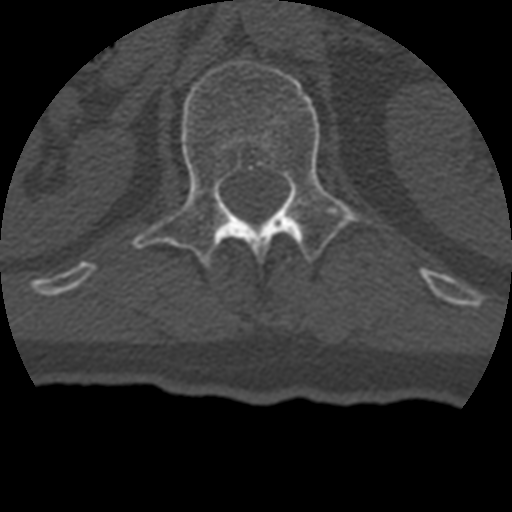
CT including the spine, one axial slice; slice 148 of 399 in the series (ordered by position); 120 kVp; bone window (W 1800 / L 400 HU); 1.25 mm slice thickness; 512 × 512 image matrix, field of view 160 × 160 mm. Patient age 69 years. Case-level facts recorded for this patient, not image findings: primary cancer: prostate.
Outlined on this slice (semi-automatic segmentation, software-assisted and operator-edited):
- L1 vertebra: bounding box <132,57,361,268> (left, top, right, bottom; pixels)